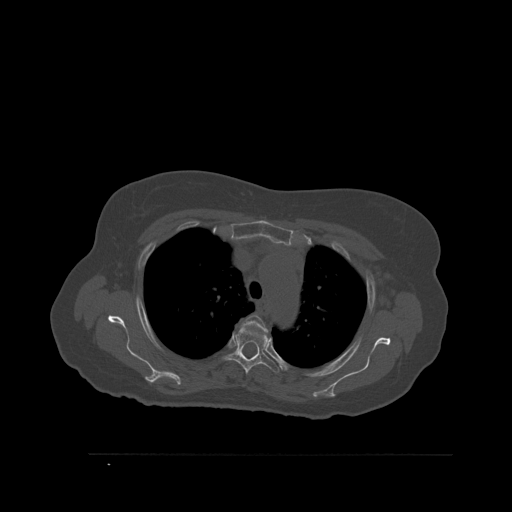
CT including the spine, one axial slice; slice 410 of 527 in the series (ordered by position); bone window (W 1800 / L 400 HU); 1.5 mm slice thickness; 512 × 512 image matrix, field of view 470 × 470 mm. Female patient, age 73 years. From the clinical record (not read from this slice): primary cancer: breast; vertebrae with lytic lesions (as recorded): L2.
Outlined on this slice (semi-automatic segmentation, software-assisted and operator-edited):
- T3 vertebra: bounding box [x1, y1, x2, y2] px = [241, 315, 267, 331]
- T4 vertebra: [225, 327, 280, 376]